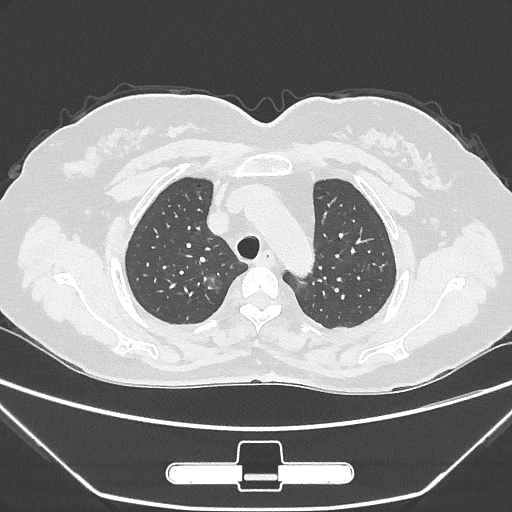
Chest CT, one axial slice. Position 224 of 275 along the scan axis. Reconstruction kernel IMR1,SharpPlus. Lung window (W 1500 / L -600 HU). 512 × 512 image matrix, field of view 356 × 356 mm. Patient: female, 63 years. From the clinical record (not read from this slice): clinical TNM (as recorded): T1a N0 M0.
Structures marked on this image (bounding box drawn by a radiologist):
- lung tumour (recorded histology: adenocarcinoma): bounding box (x1, y1, x2, y2) in pixels: (202, 270, 233, 304)